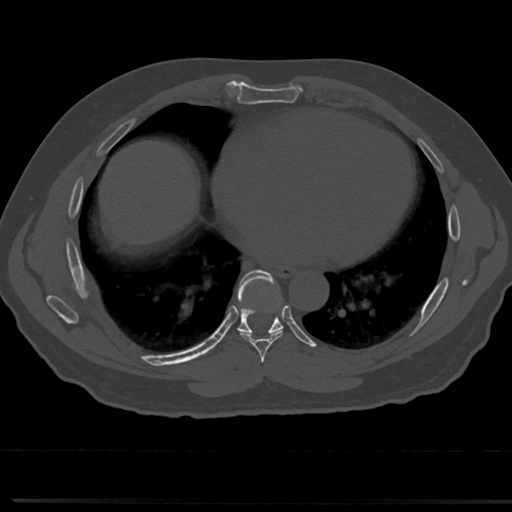
CT including the spine, one axial slice; slice 382 of 817 in the series (ordered by position); 120 kVp; bone window (W 1800 / L 400 HU); 512 × 512 image matrix. Male patient, age 61 years. From the clinical record (not read from this slice): primary cancer: prostate.
Annotated regions visible in this slice (semi-automatic segmentation, software-assisted and operator-edited):
- T6 vertebra: box from (x=260, y=368) to (x=267, y=377) px
- T7 vertebra: (x=229, y=273)–(x=306, y=352)